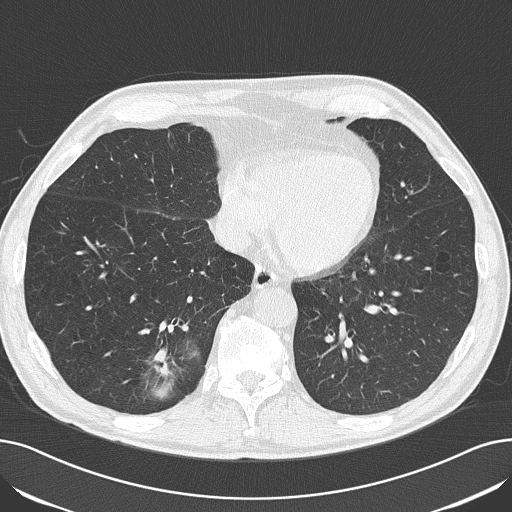
Low-dose screening chest CT, axial slice; baseline annual screen; lung window (W 1500 / L -600 HU); lung (sharp) reconstruction kernel (B50f); slice 125 of 182 in the series. Male participant, aged 71 years at enrolment. Current smoker at enrolment.
Expert reader's lesion annotation, box from (x=133, y=332) to (x=195, y=399) px. Screening reader's record for this exam (one nodule recorded; not confirmed to be the boxed lesion): non-calcified nodule or mass ≥4 mm, right lower lobe, 14 × 14 mm, spiculated (stellate) margins, soft tissue attenuation. Official screen result: positive, change unspecified: nodule(s) >= 4 mm or enlarging nodule(s), mass(es), or other non-specific abnormalities suspicious for lung cancer. Later outcome: lung cancer diagnosed 145 days after this screen — adenocarcinoma, NOS, right lower lobe, moderately differentiated (G2), stage IA (AJCC 6th edition), 24 mm at pathology.